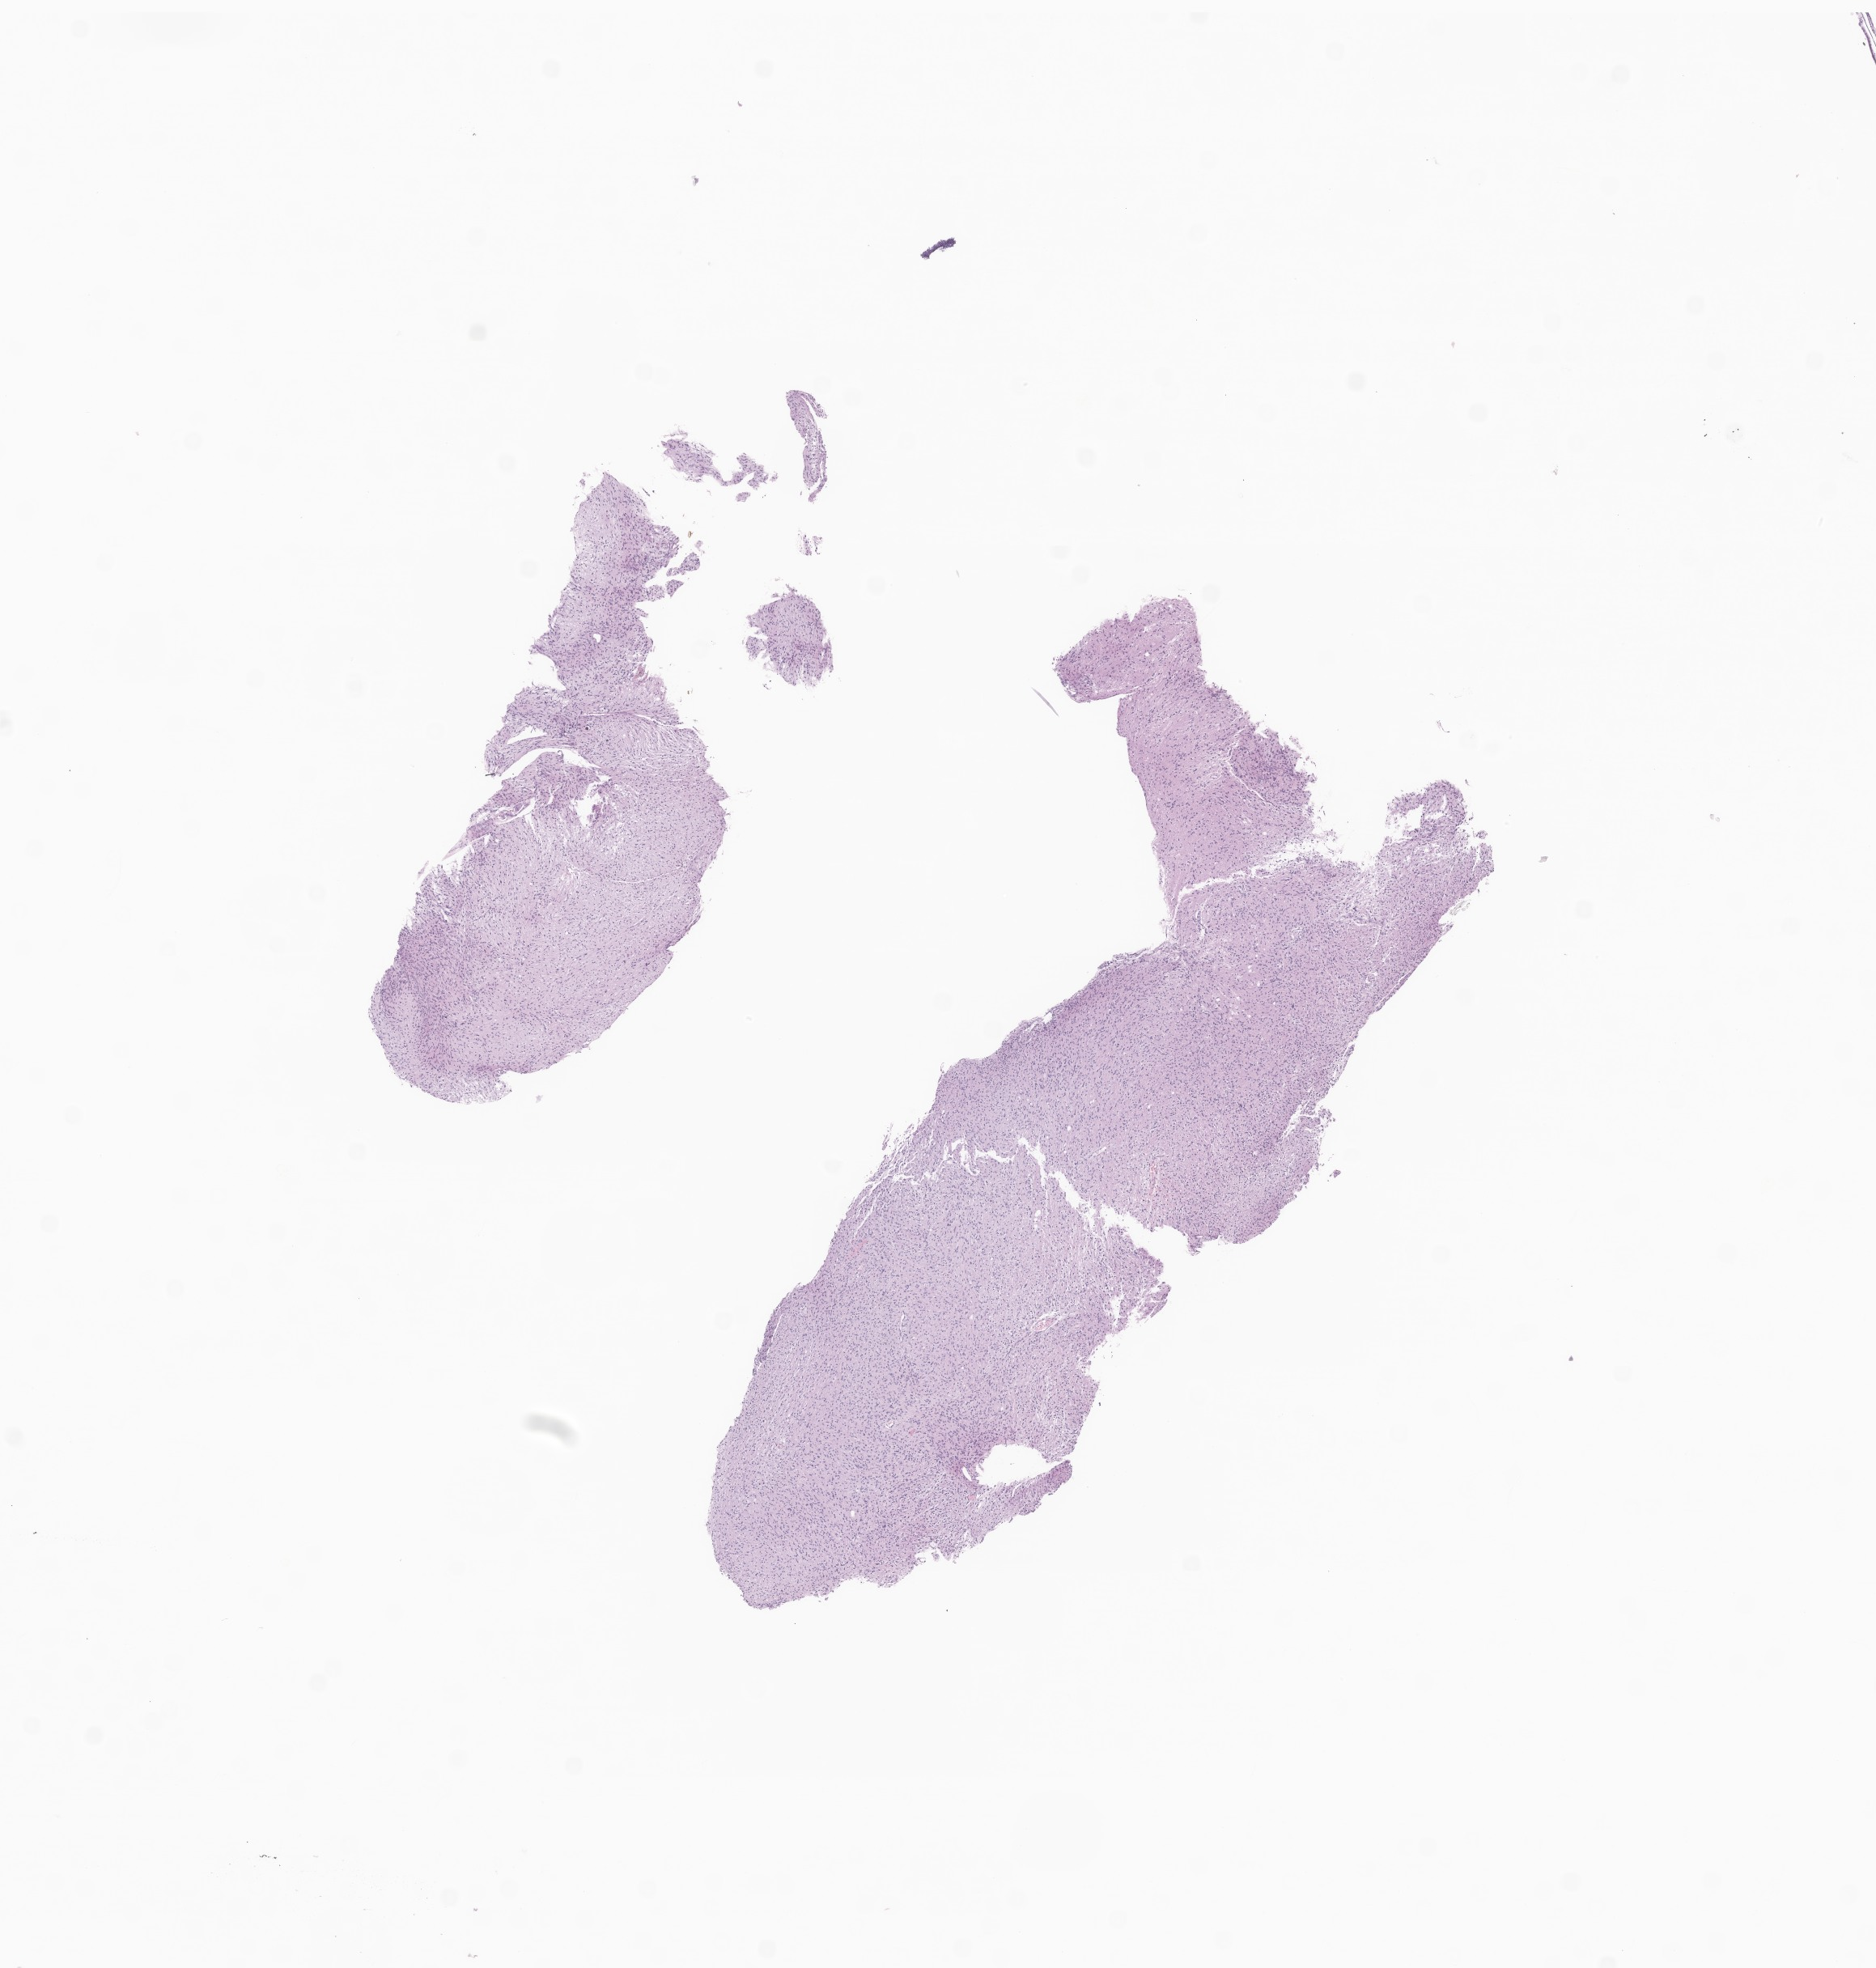
Whole-slide image, haematoxylin and eosin stain of tumor tissue from the frontal lobe — shown as a low-resolution overview of the whole scanned area (about 9.8 x 10.3 mm); formalin-fixed, paraffin-embedded (FFPE) tissue. Male patient, age 165 months.
Recorded diagnosis: Pleomorphic xanthoastrocytoma, NOS.